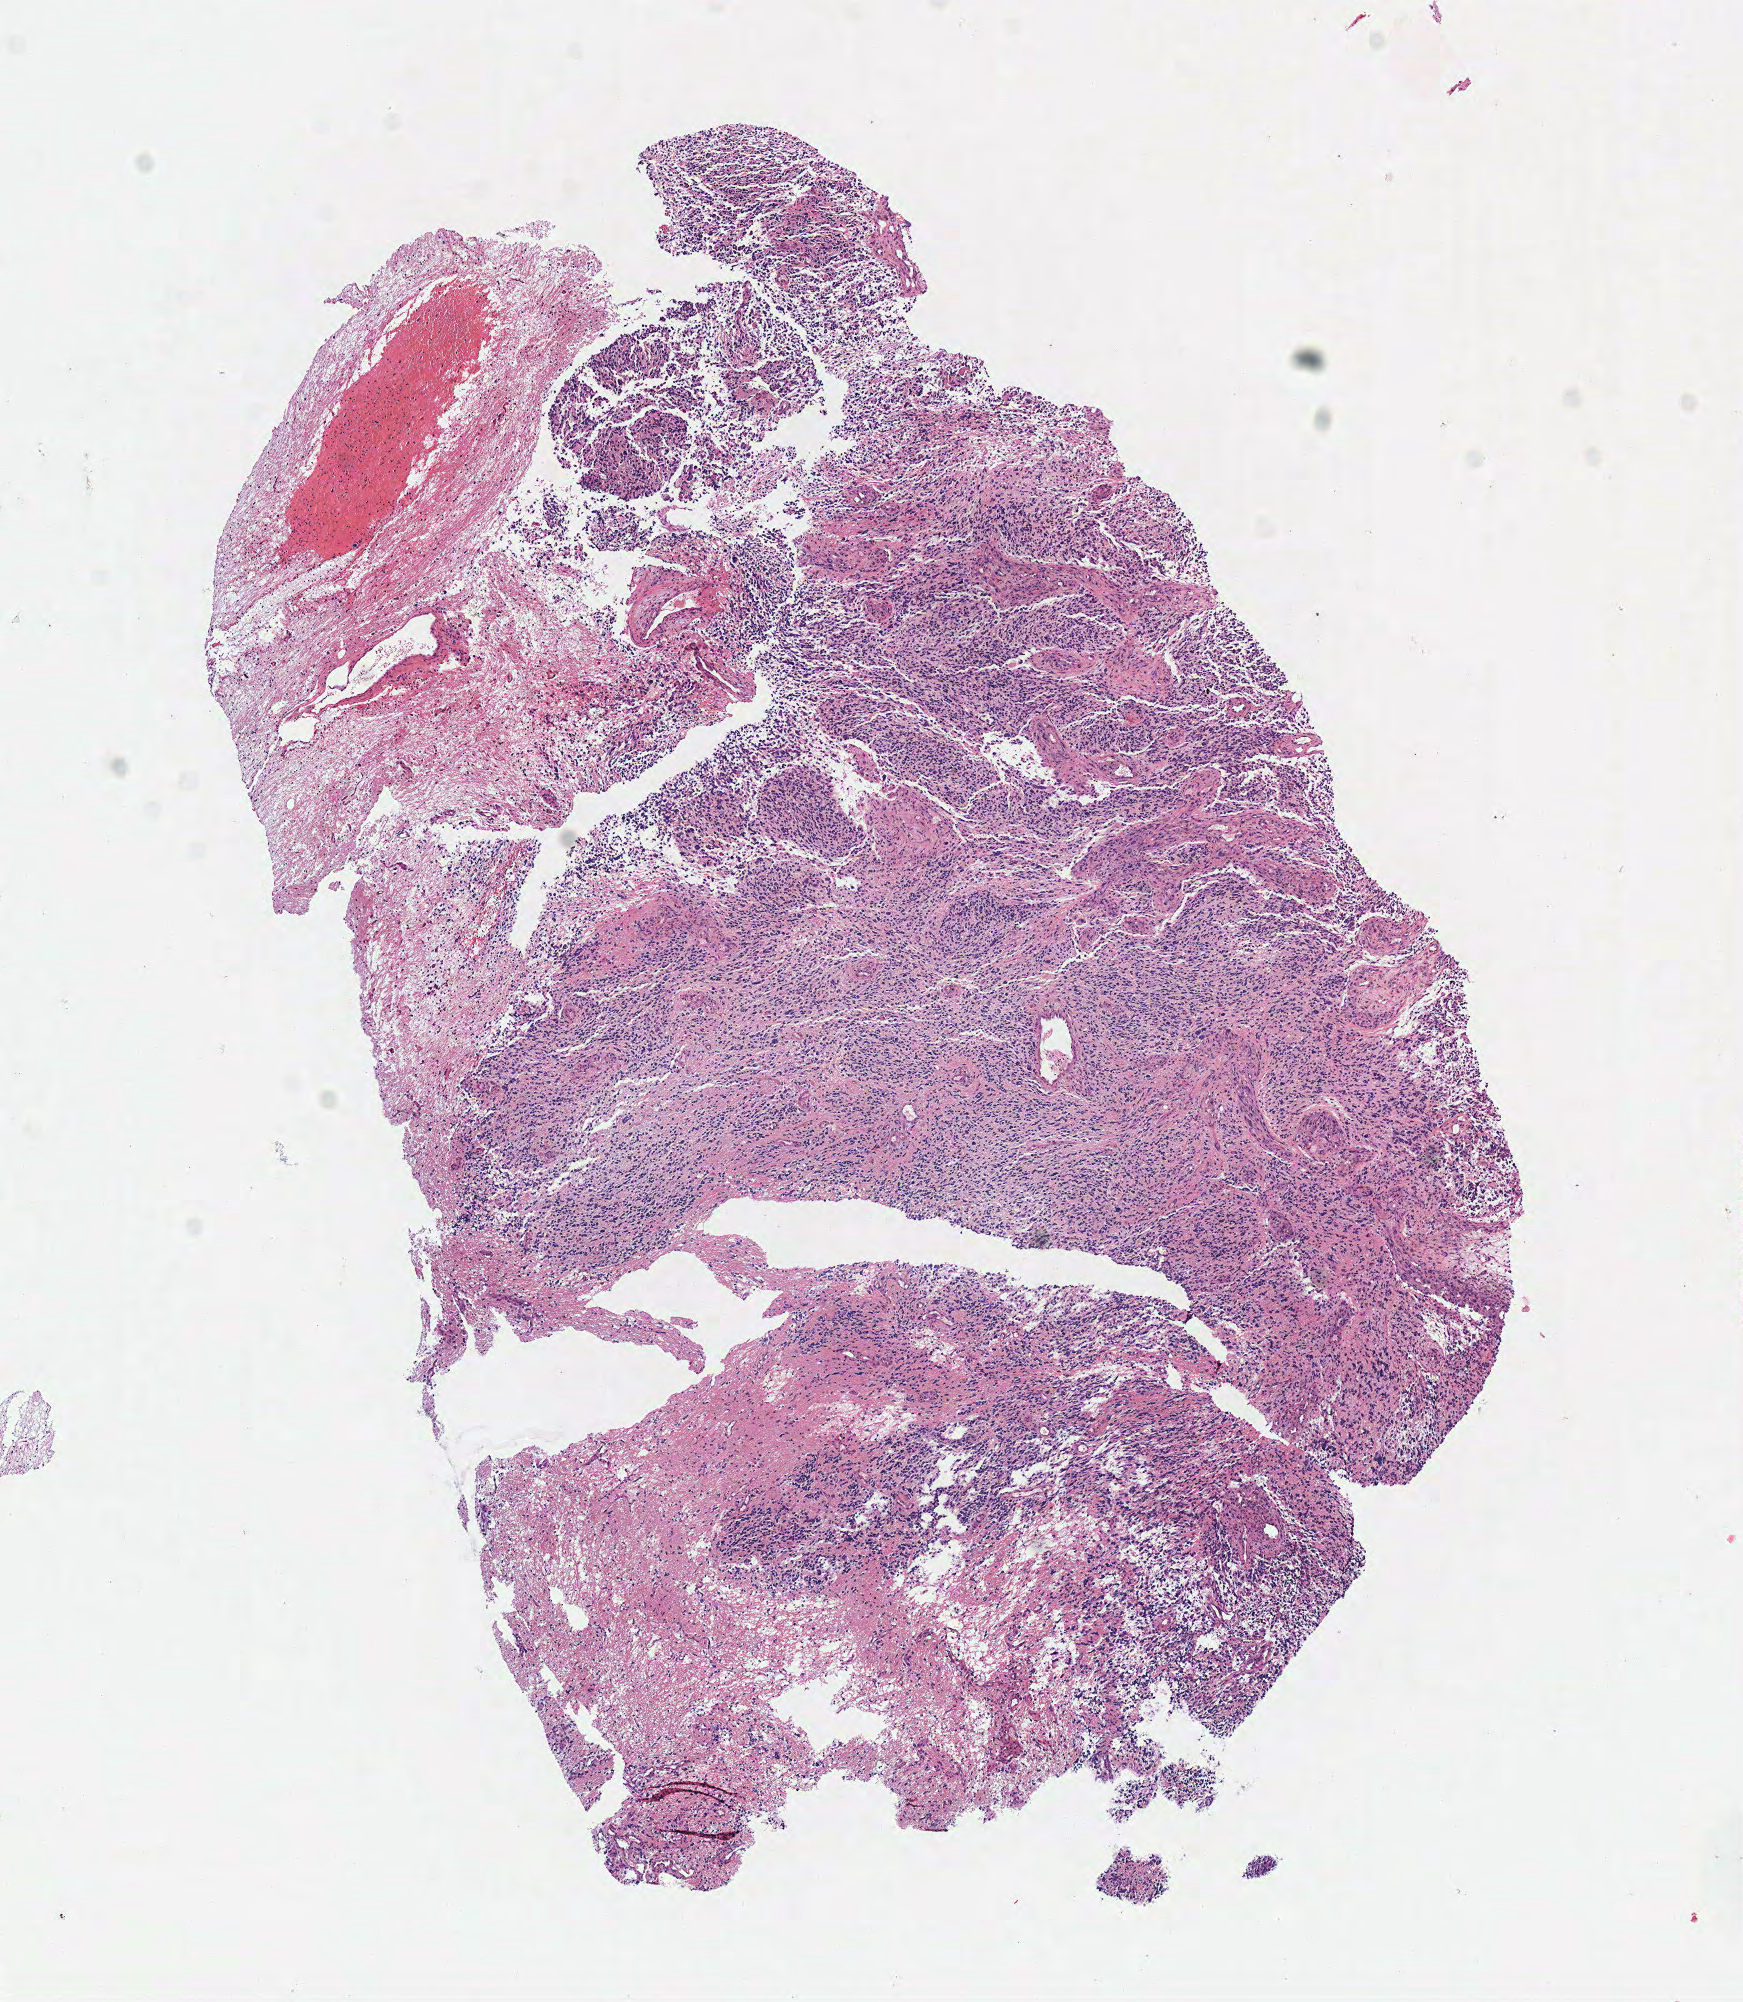
Digitized H&E tissue section (whole slide) — low-resolution overview of the scanned area, about 6.9 x 7.9 mm (from a 40x scan), frozen section from the top of the tissue portion, primary tumour sample from the brain. Female, age 76 years at initial diagnosis. Slide review estimates, as recorded: tumour cells 100%, tumour nuclei 80%, normal cells 0%, stromal cells 0%, necrosis 0%.
Pathologic diagnosis: Glioblastoma.